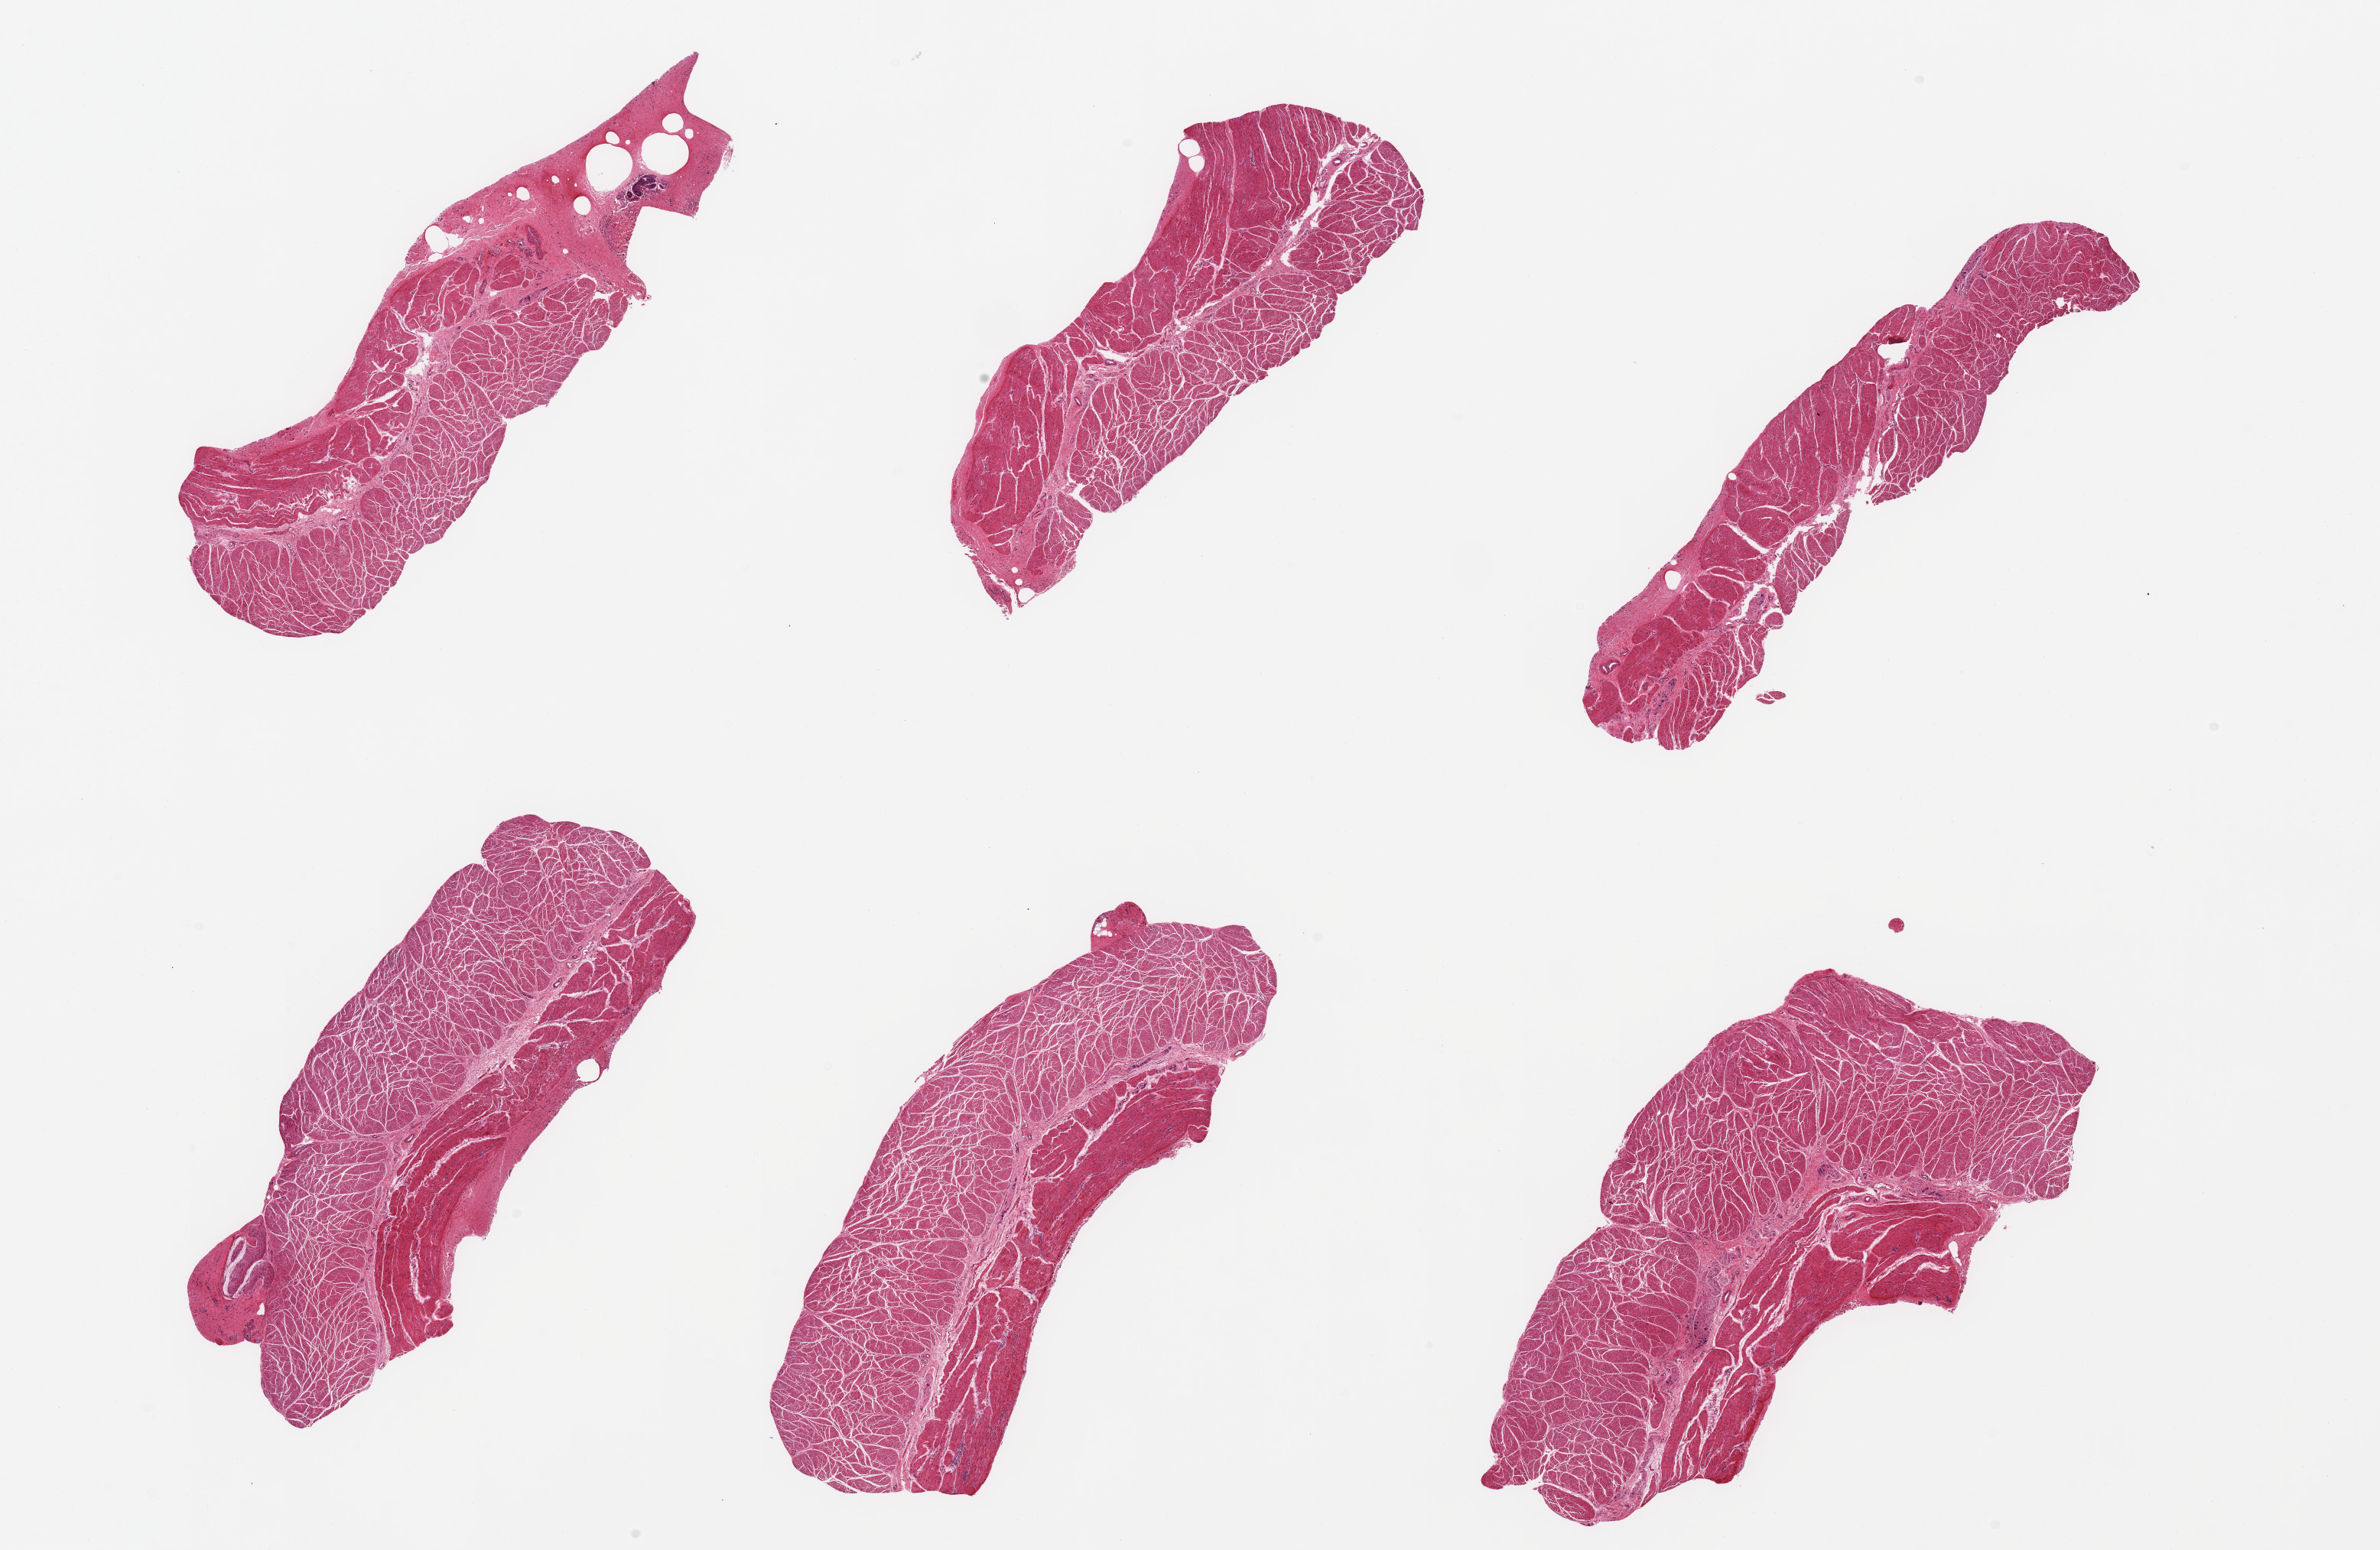
Whole-slide image, haematoxylin and eosin stain — whole scanned area (about 24.6 x 16.0 mm) shown as a low-resolution overview. PAXgene-fixed, paraffin-embedded tissue. Sampled site (target tissue): esophageal muscle. Tissue donor sample. Donor sex: female.
Review note (as recorded): 6 pieces; target muscularis persent.